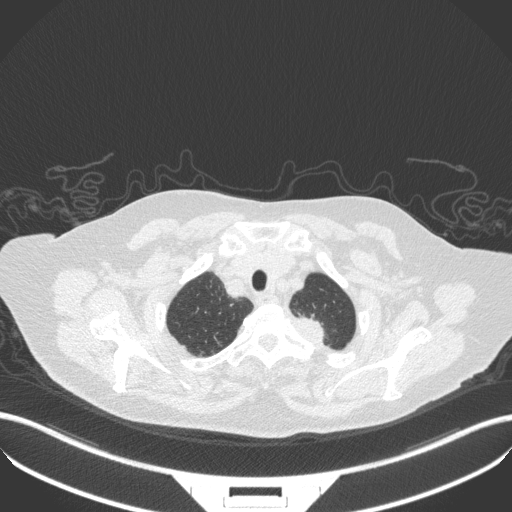
Chest CT, one axial slice. Slice 307 of 353 in the series (ordered by position). Reconstruction kernel B31f. 100 kVp. Lung window (W 1500 / L -600 HU). 512 × 512 image matrix, field of view 400 × 400 mm. Female patient, age 81 years. From the clinical record (not read from this slice): clinical TNM (as recorded): T2a N0 M0.
Structures marked on this image (rectangle marked by the reading radiologist):
- lung tumour (recorded histology: adenocarcinoma): bounding box <293,309,338,353> (left, top, right, bottom; pixels)